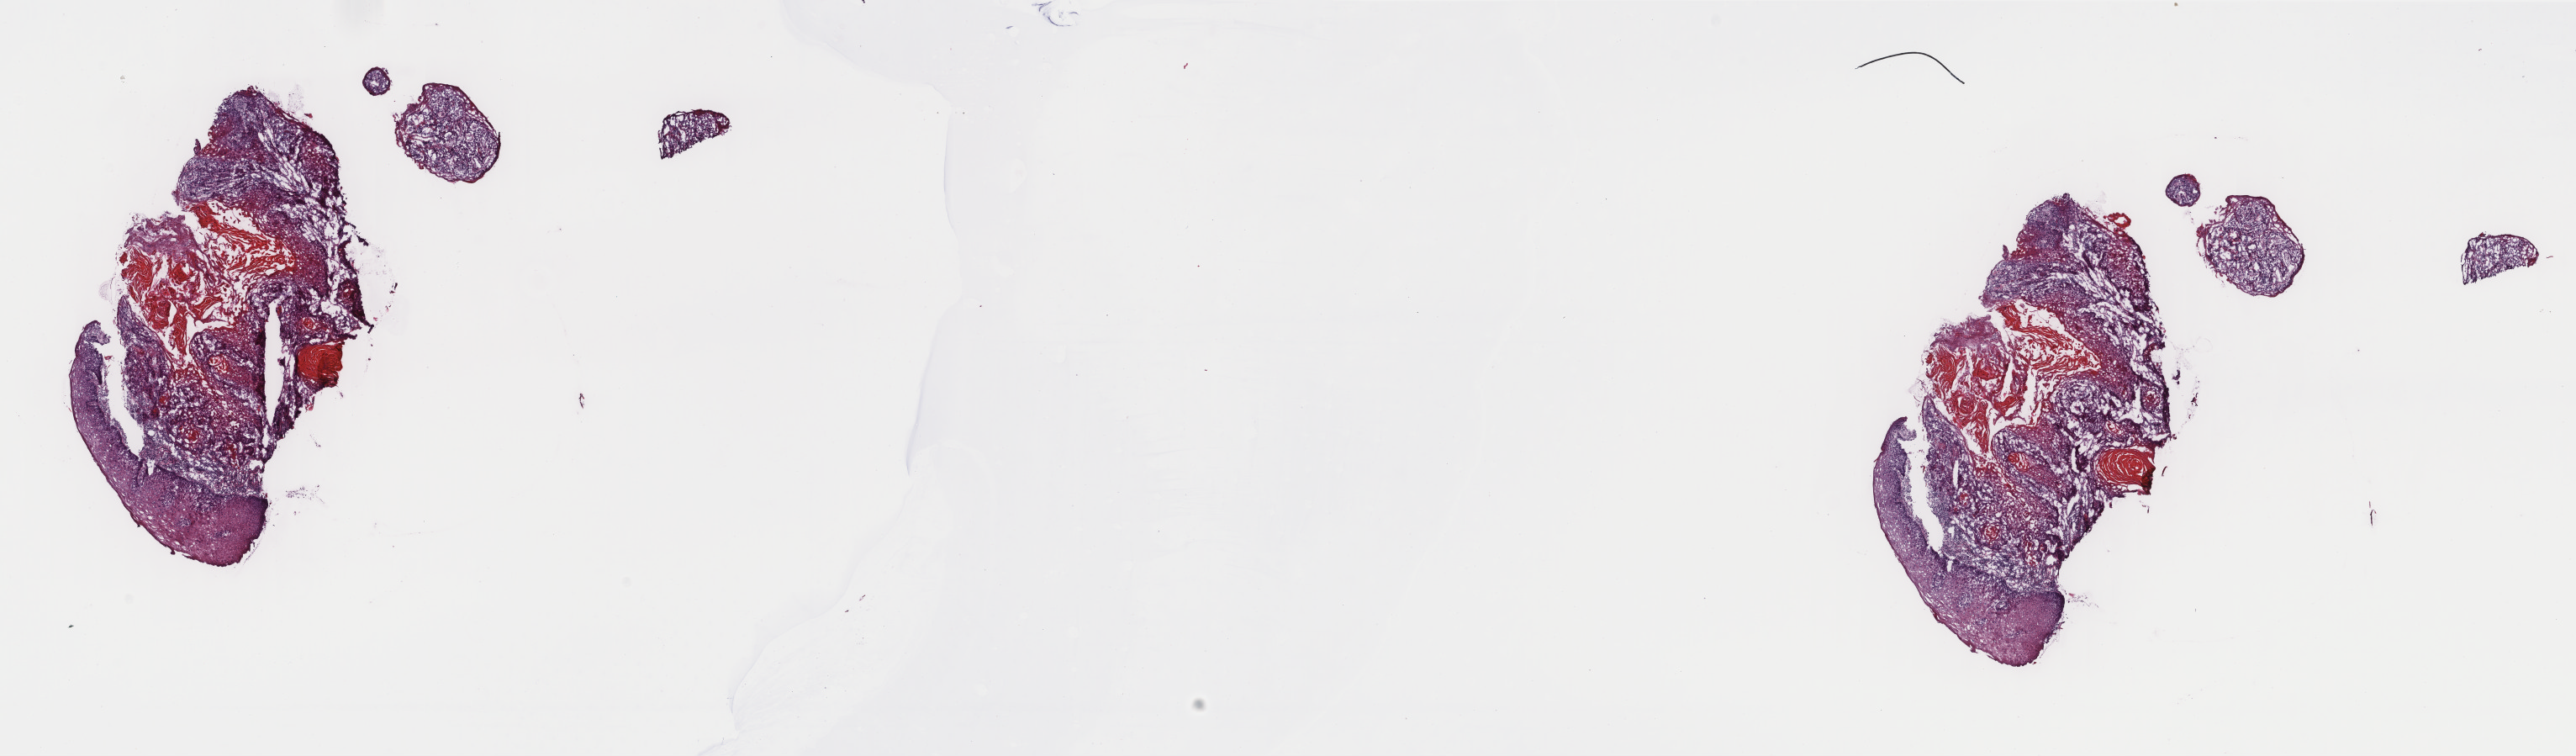
Digitized H&E tissue section (whole slide) — a low-resolution overview of the entire scanned area, about 24.3 x 7.1 mm (slide scanned at 40x), frozen section from the top of the tissue portion, primary tumour sample from the head and neck. Patient: male, age at initial diagnosis 24 years. Histologic grade: G1 (well differentiated). Pathologist review of this section (percent, as recorded): tumour cells 80%, tumour nuclei 75%, normal cells 20%, stromal cells 0%, necrosis 0%. Inflammatory infiltration, as recorded: lymphocyte infiltration 4%, monocyte infiltration 0%, neutrophil infiltration 0%.
* diagnosis: Squamous cell carcinoma, NOS (tongue, NOS)
* laterality: right
* AJCC pathologic stage: III